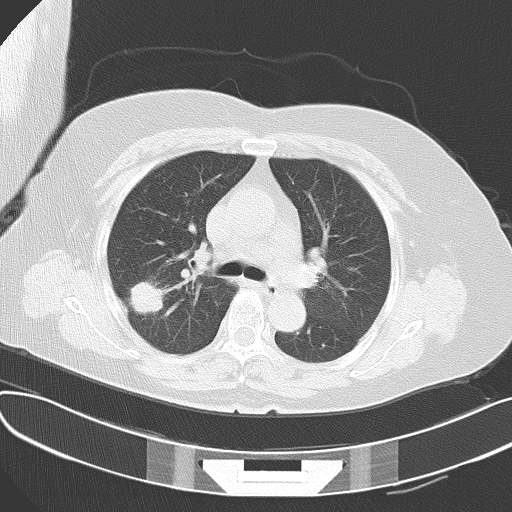
Chest CT, one axial slice; position 45 of 61 along the scan axis; reconstruction kernel B70f; 120 kVp; lung window (W 1500 / L -600 HU); 5 mm slice thickness; 512 × 512 image matrix, field of view 367 × 367 mm. Patient: female, 63 years. Case-level facts recorded for this patient, not image findings: clinical TNM (as recorded): T1c N3 M1a.
Outlined on this slice (rectangle marked by the reading radiologist):
- lung tumour (recorded histology: adenocarcinoma): box from (x=124, y=277) to (x=172, y=338) px